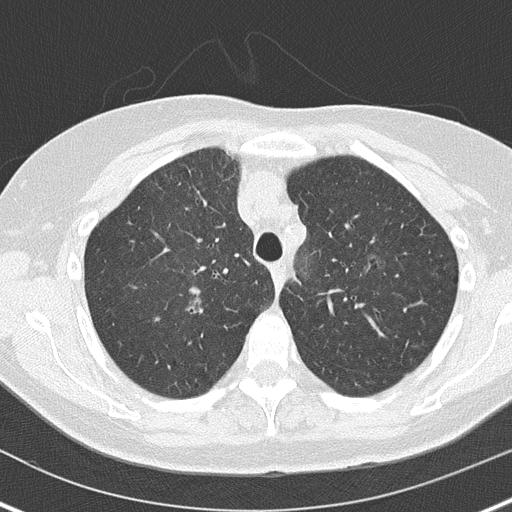
Chest CT (low-dose screening protocol), one axial image; baseline annual screen; lung window (W 1500 / L -600 HU); 120 kVp. Female participant, aged 61 years at enrolment. Current smoker at enrolment.
- Lesion marked by an expert reader, bounding box [x1, y1, x2, y2] px = [176, 285, 222, 325].
- Screening reader's record for this exam (one nodule recorded; not confirmed to be the boxed lesion): non-calcified nodule or mass ≥4 mm, right upper lobe, 8 × 5 mm, smooth margins, soft tissue attenuation.
- Official screen result: positive, change unspecified: nodule(s) >= 4 mm or enlarging nodule(s), mass(es), or other non-specific abnormalities suspicious for lung cancer.